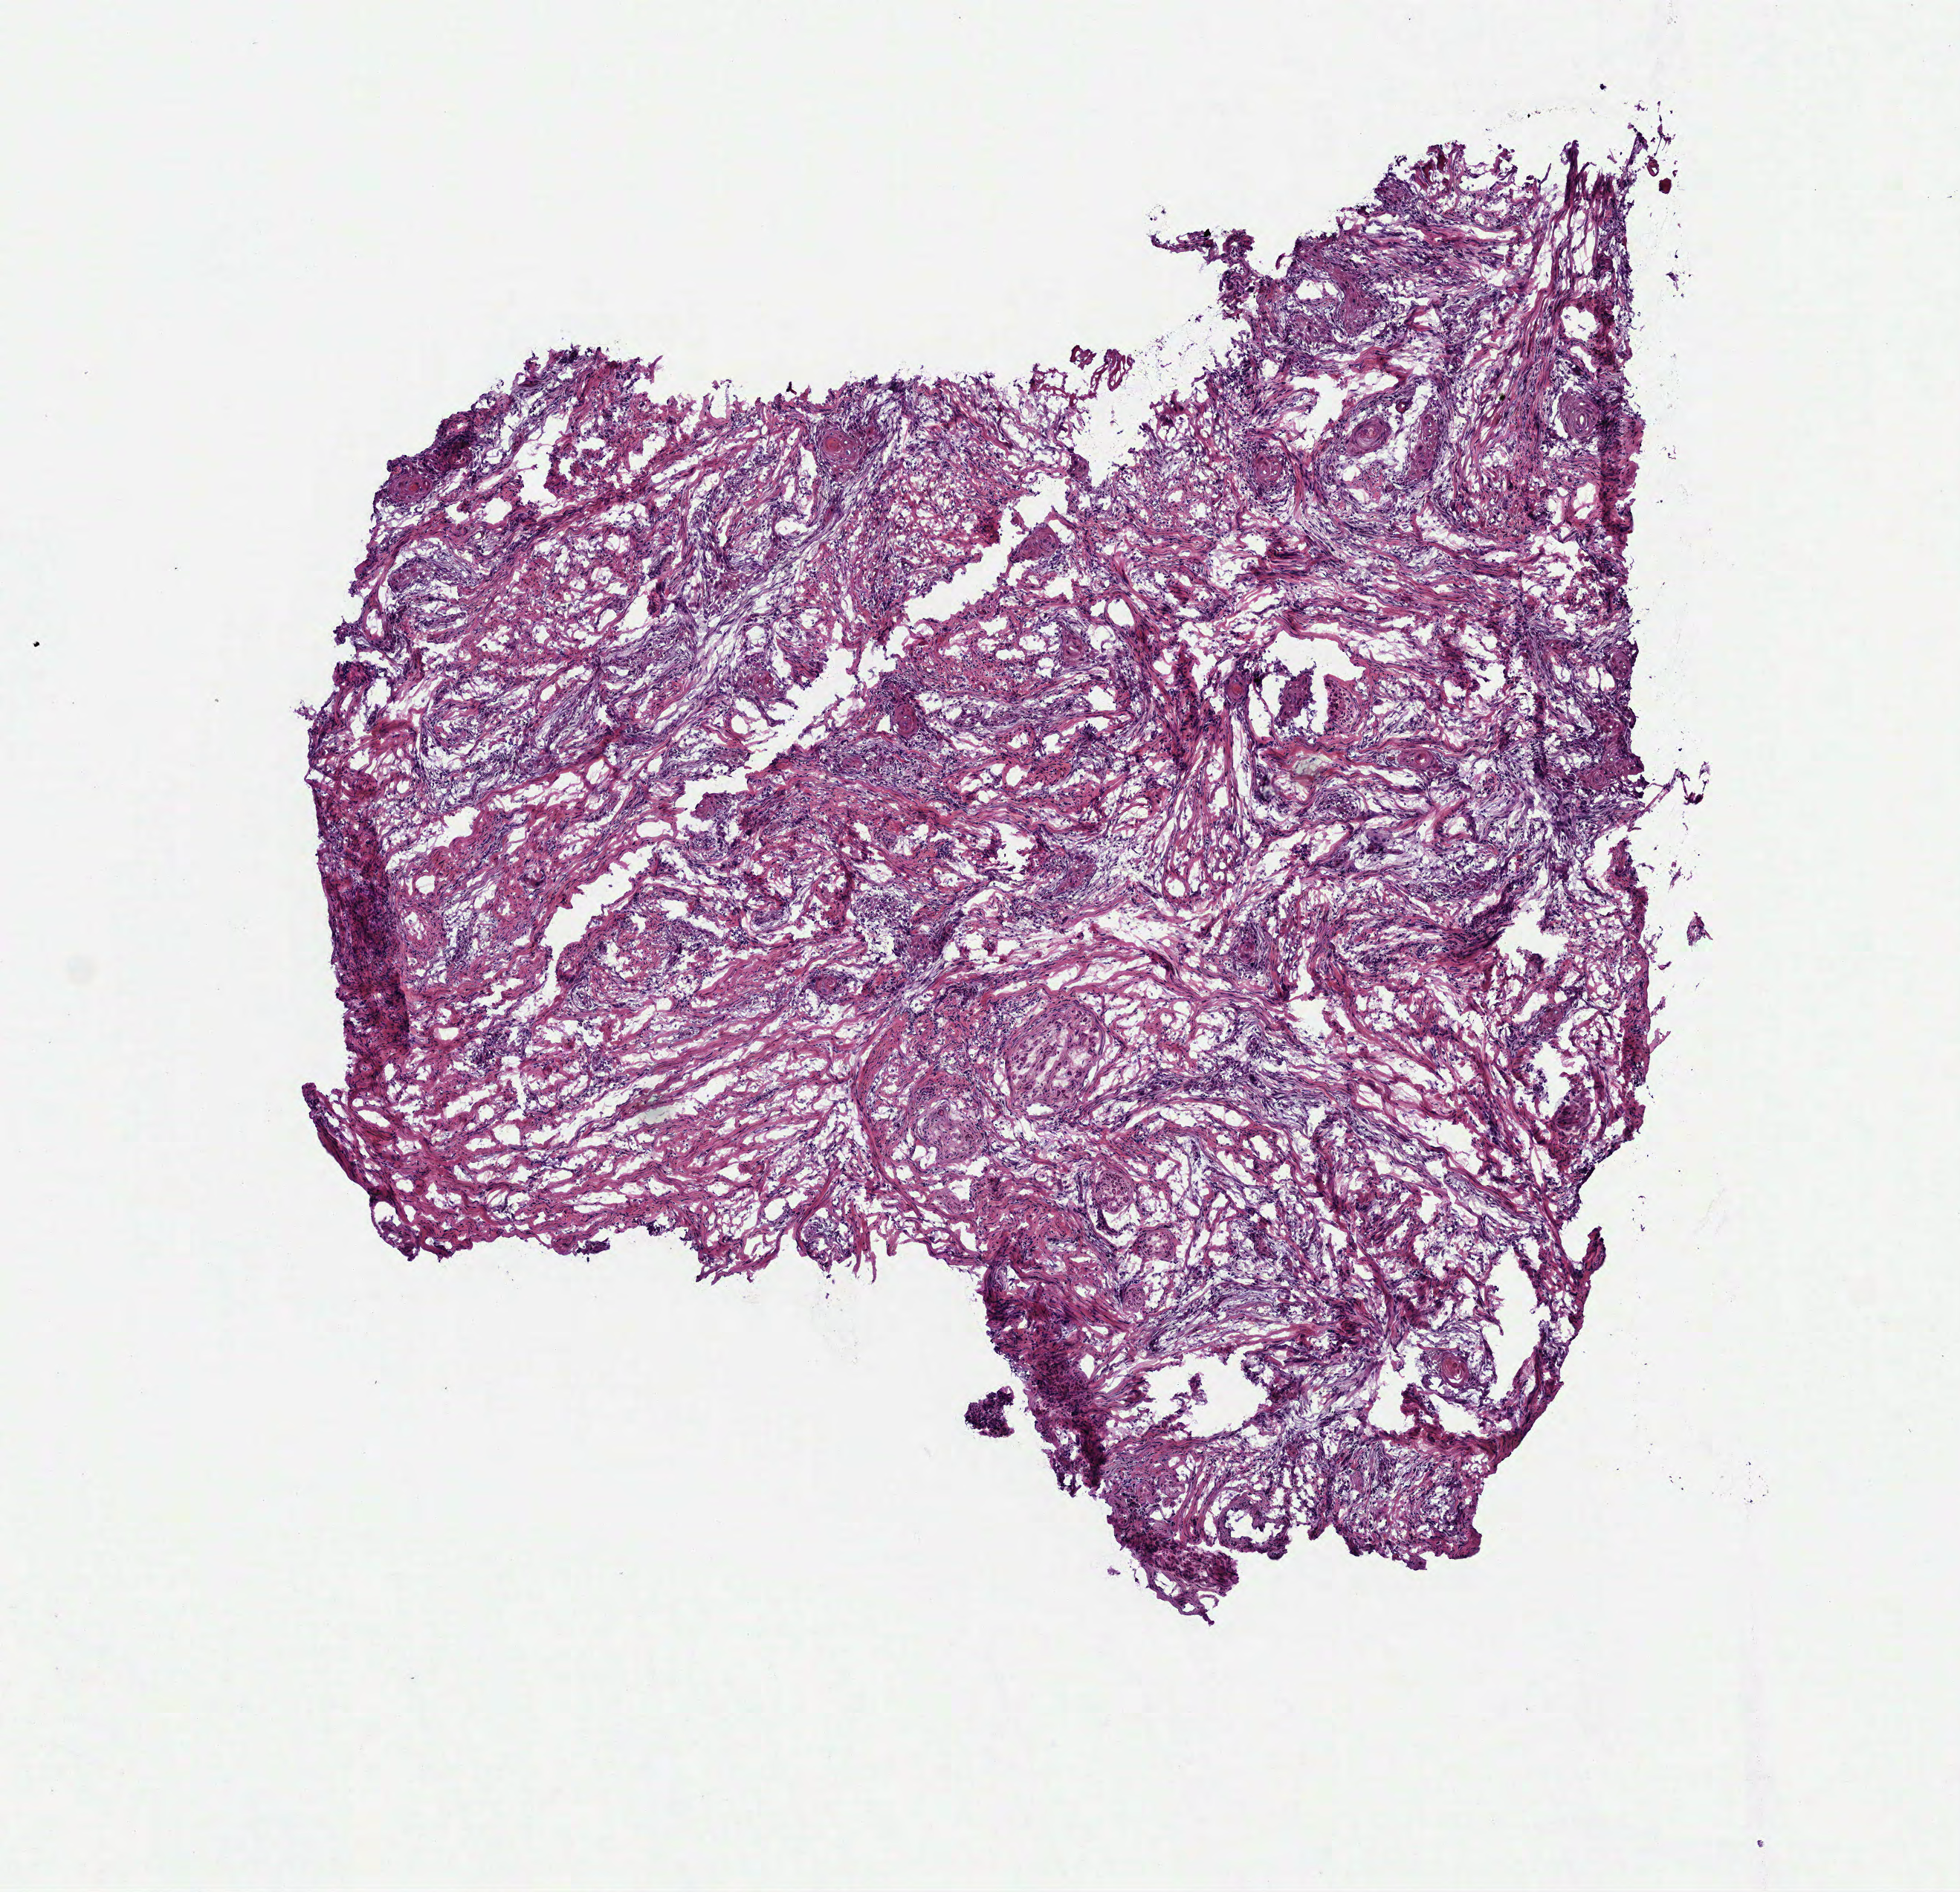
H&E whole-slide image — low-resolution overview of the scanned area, about 5.3 x 5.1 mm (slide scanned at 40x), frozen section from the top of the tissue portion, sample: primary tumour, head and neck. Male, age 64 years at initial diagnosis. Histologic grade: G2 (moderately differentiated). Composition of this section per pathologist review: tumour cells 75%, tumour nuclei 65%, normal cells 0%, stromal cells 25%, necrosis 0%.
Diagnosis: Squamous cell carcinoma, NOS (tongue, NOS). AJCC pathologic stage: IVA (7th edition). Lymph nodes positive (case pathology): 1 of 75 examined. TNM: T4a N1.